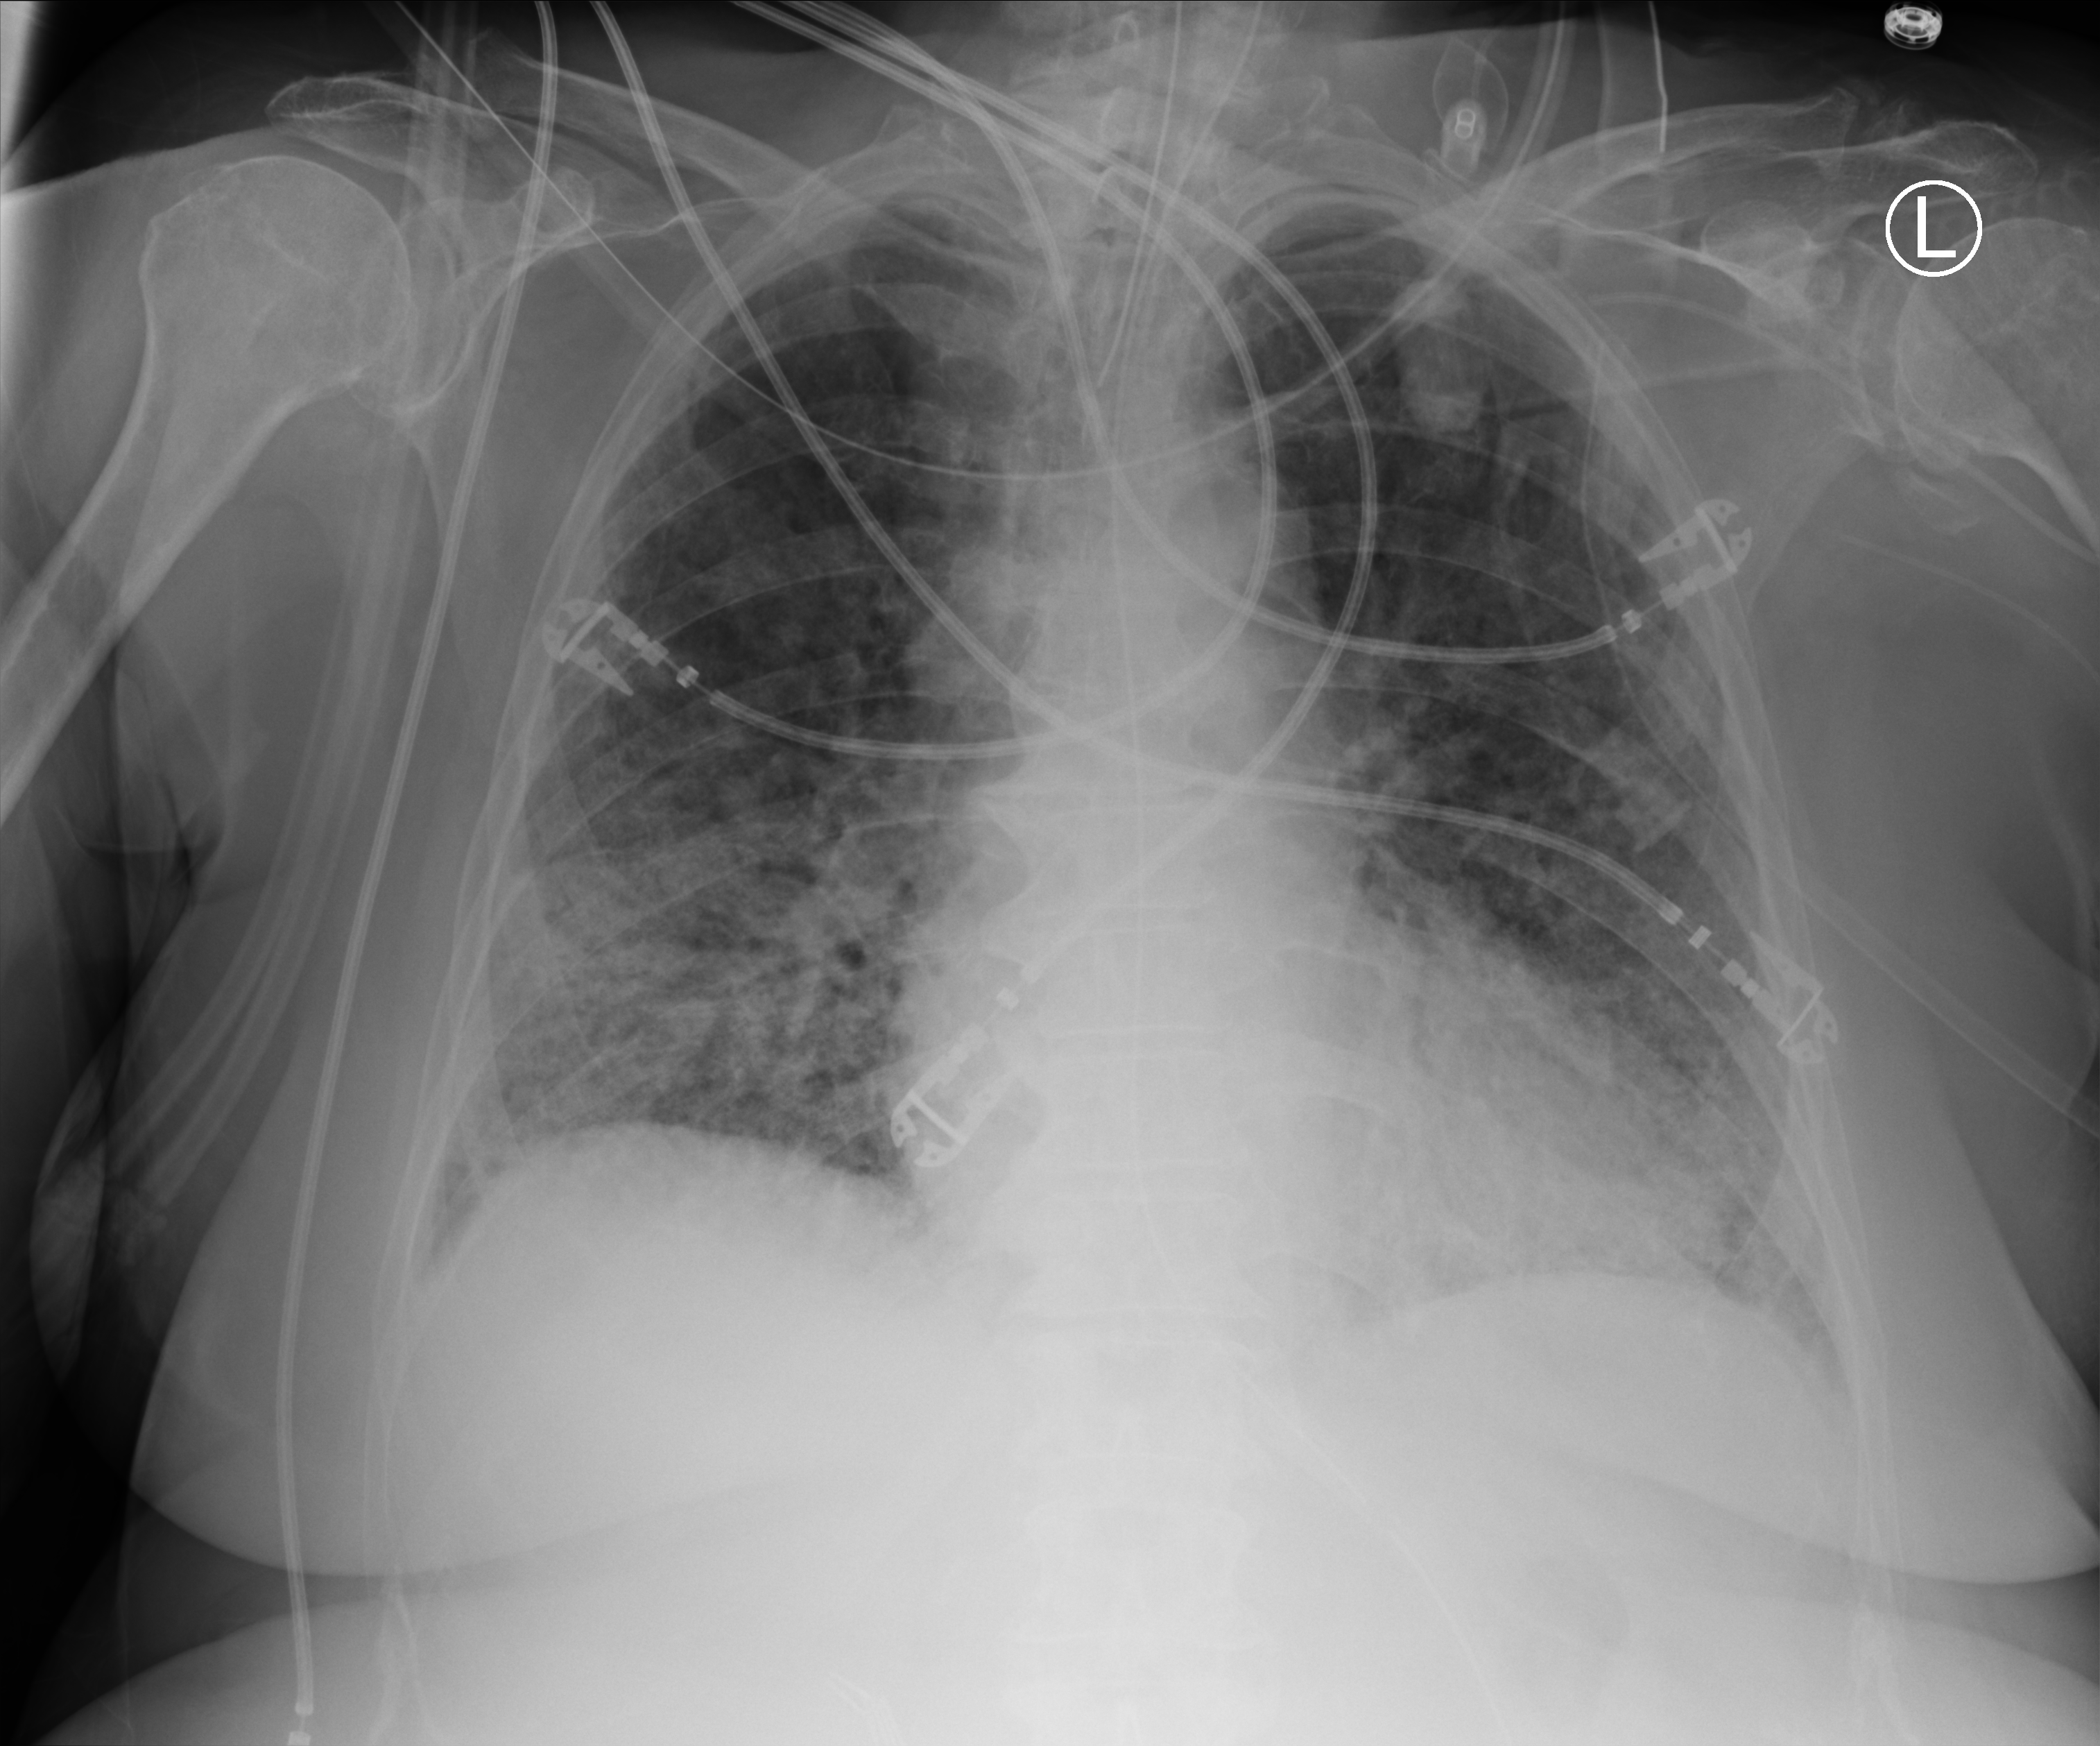
Bedside chest radiograph (computed radiography). Female patient hospitalised with COVID-19, age 75–90 years.
From the hospital-stay record, not from the radiograph (when in the stay this image was taken is not recorded): admitted to intensive care during this hospital stay: no; length of hospital stay: 56 days.